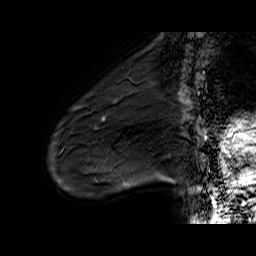
Breast MRI (dynamic contrast-enhanced), one sagittal slice. Slice 13 of 60 in the series (ordered by position). Dynamic contrast-enhanced series, time point 2 of 6 at this slice position (early post-contrast). 1.5 T. TE 6.5 ms, TR 32.9 ms. 4 mm slice thickness. 256 × 256 image matrix. Female patient. Case-level facts recorded for this patient, not image findings: setting: breast cancer imaged before/during neoadjuvant chemotherapy; receptor status: HER2-positive.
Annotated regions visible in this slice (semi-automatically segmented with operator editing):
- analysis volume of interest (the breast-tissue region the enhancement analysis was run in; not a lesion): bounding box [x1, y1, x2, y2] px = [72, 88, 133, 137]
- tumour enhancement mask (voxels above the 100 % enhancement threshold inside the analysis volume of interest): [73, 101, 116, 121]